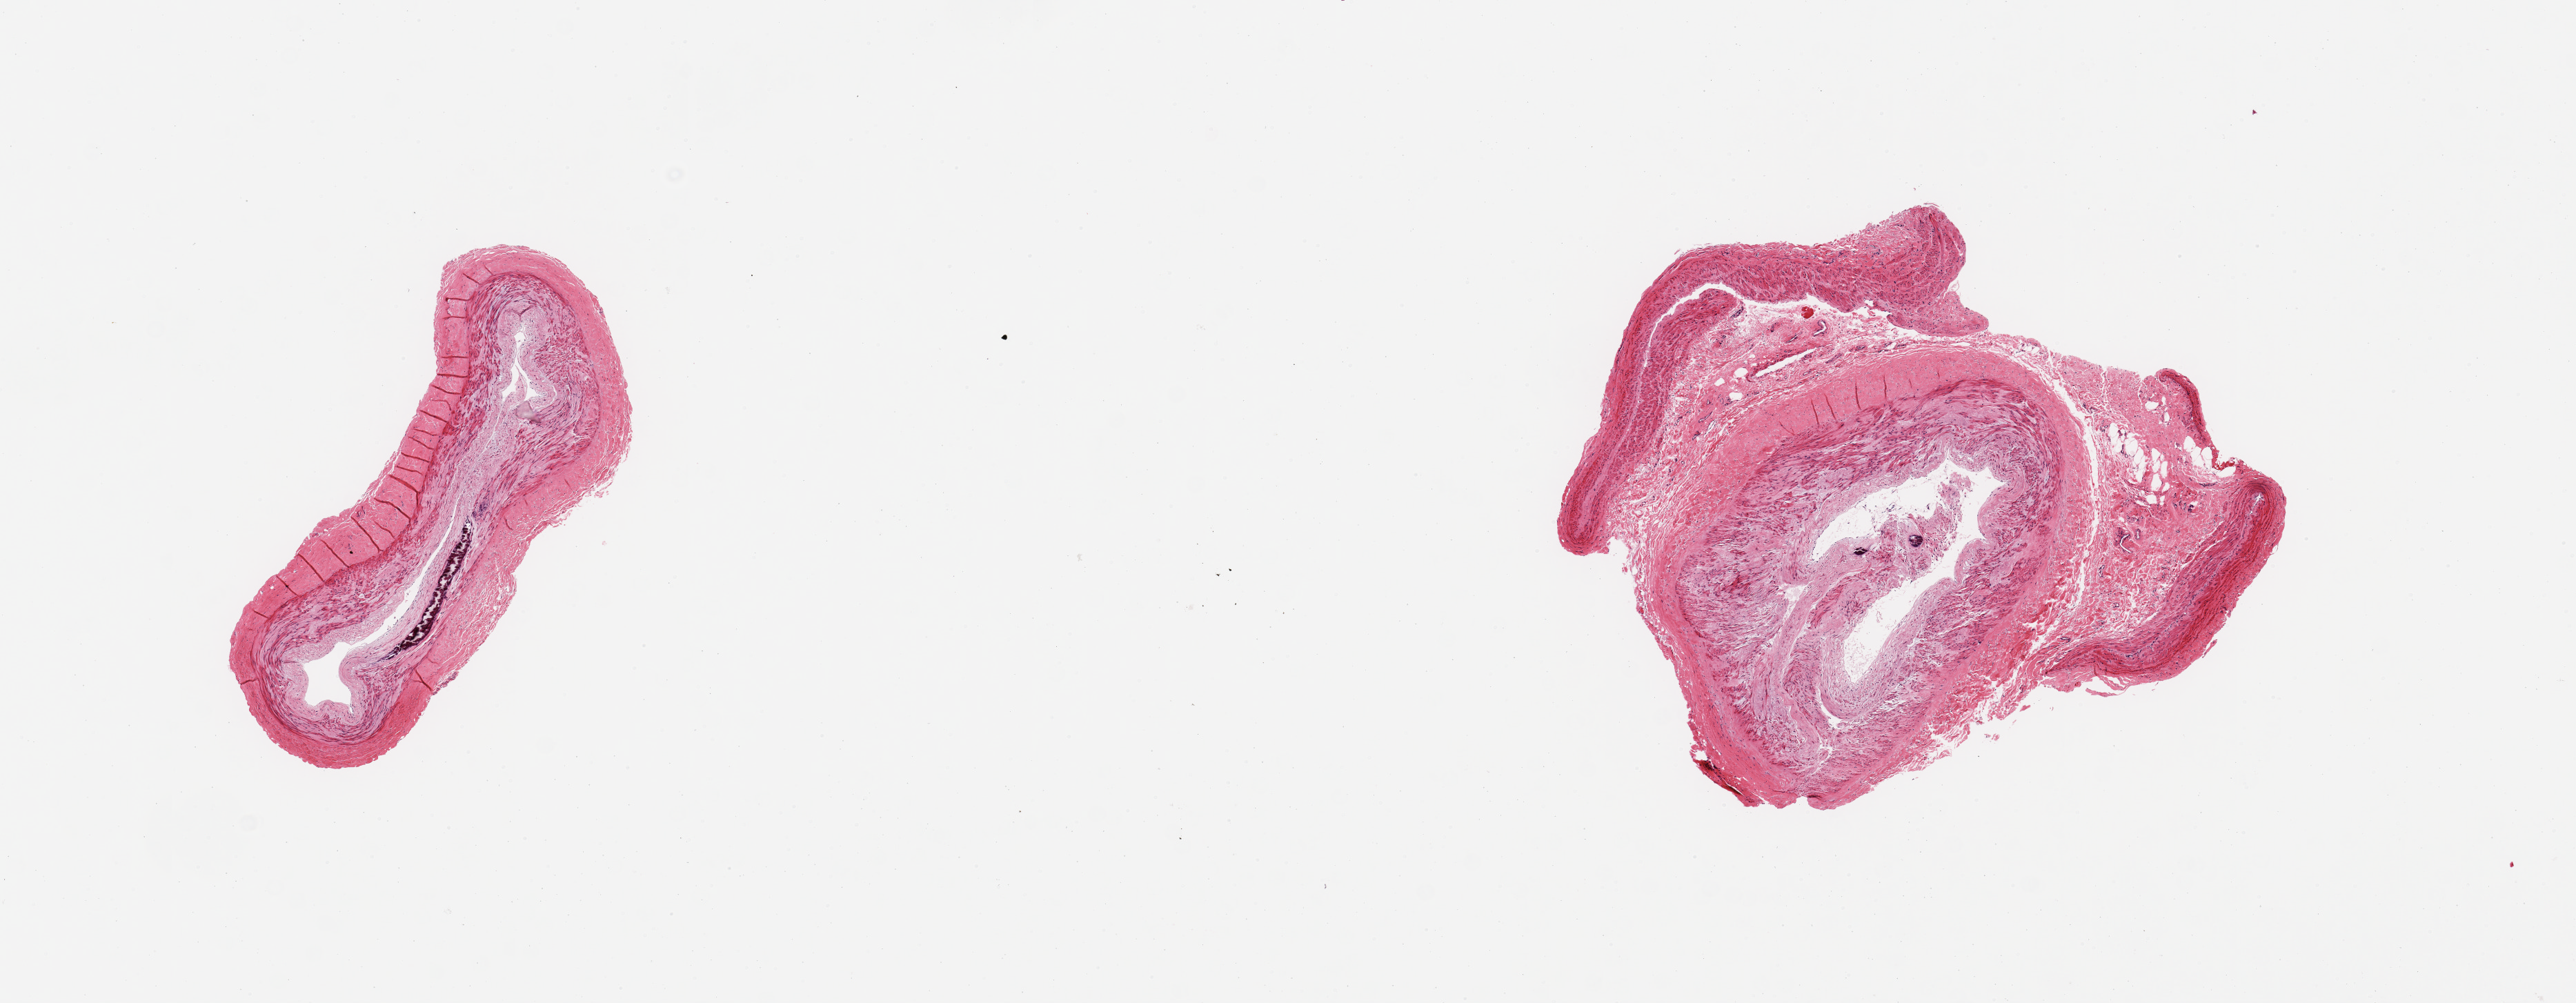
Digitized H&E-stained section, brightfield, whole scanned area (about 14.8 x 5.7 mm, from a 20x scan) shown as a low-resolution overview; PAXgene-fixed paraffin-embedded (PFPE) section; sampled site (target tissue): tibial artery; tissue donor sample. Female donor.
Pathologist's review note for this sample: 2 pieces; medial calcifications; intimal accentuation likely early fibrous plaque formation.